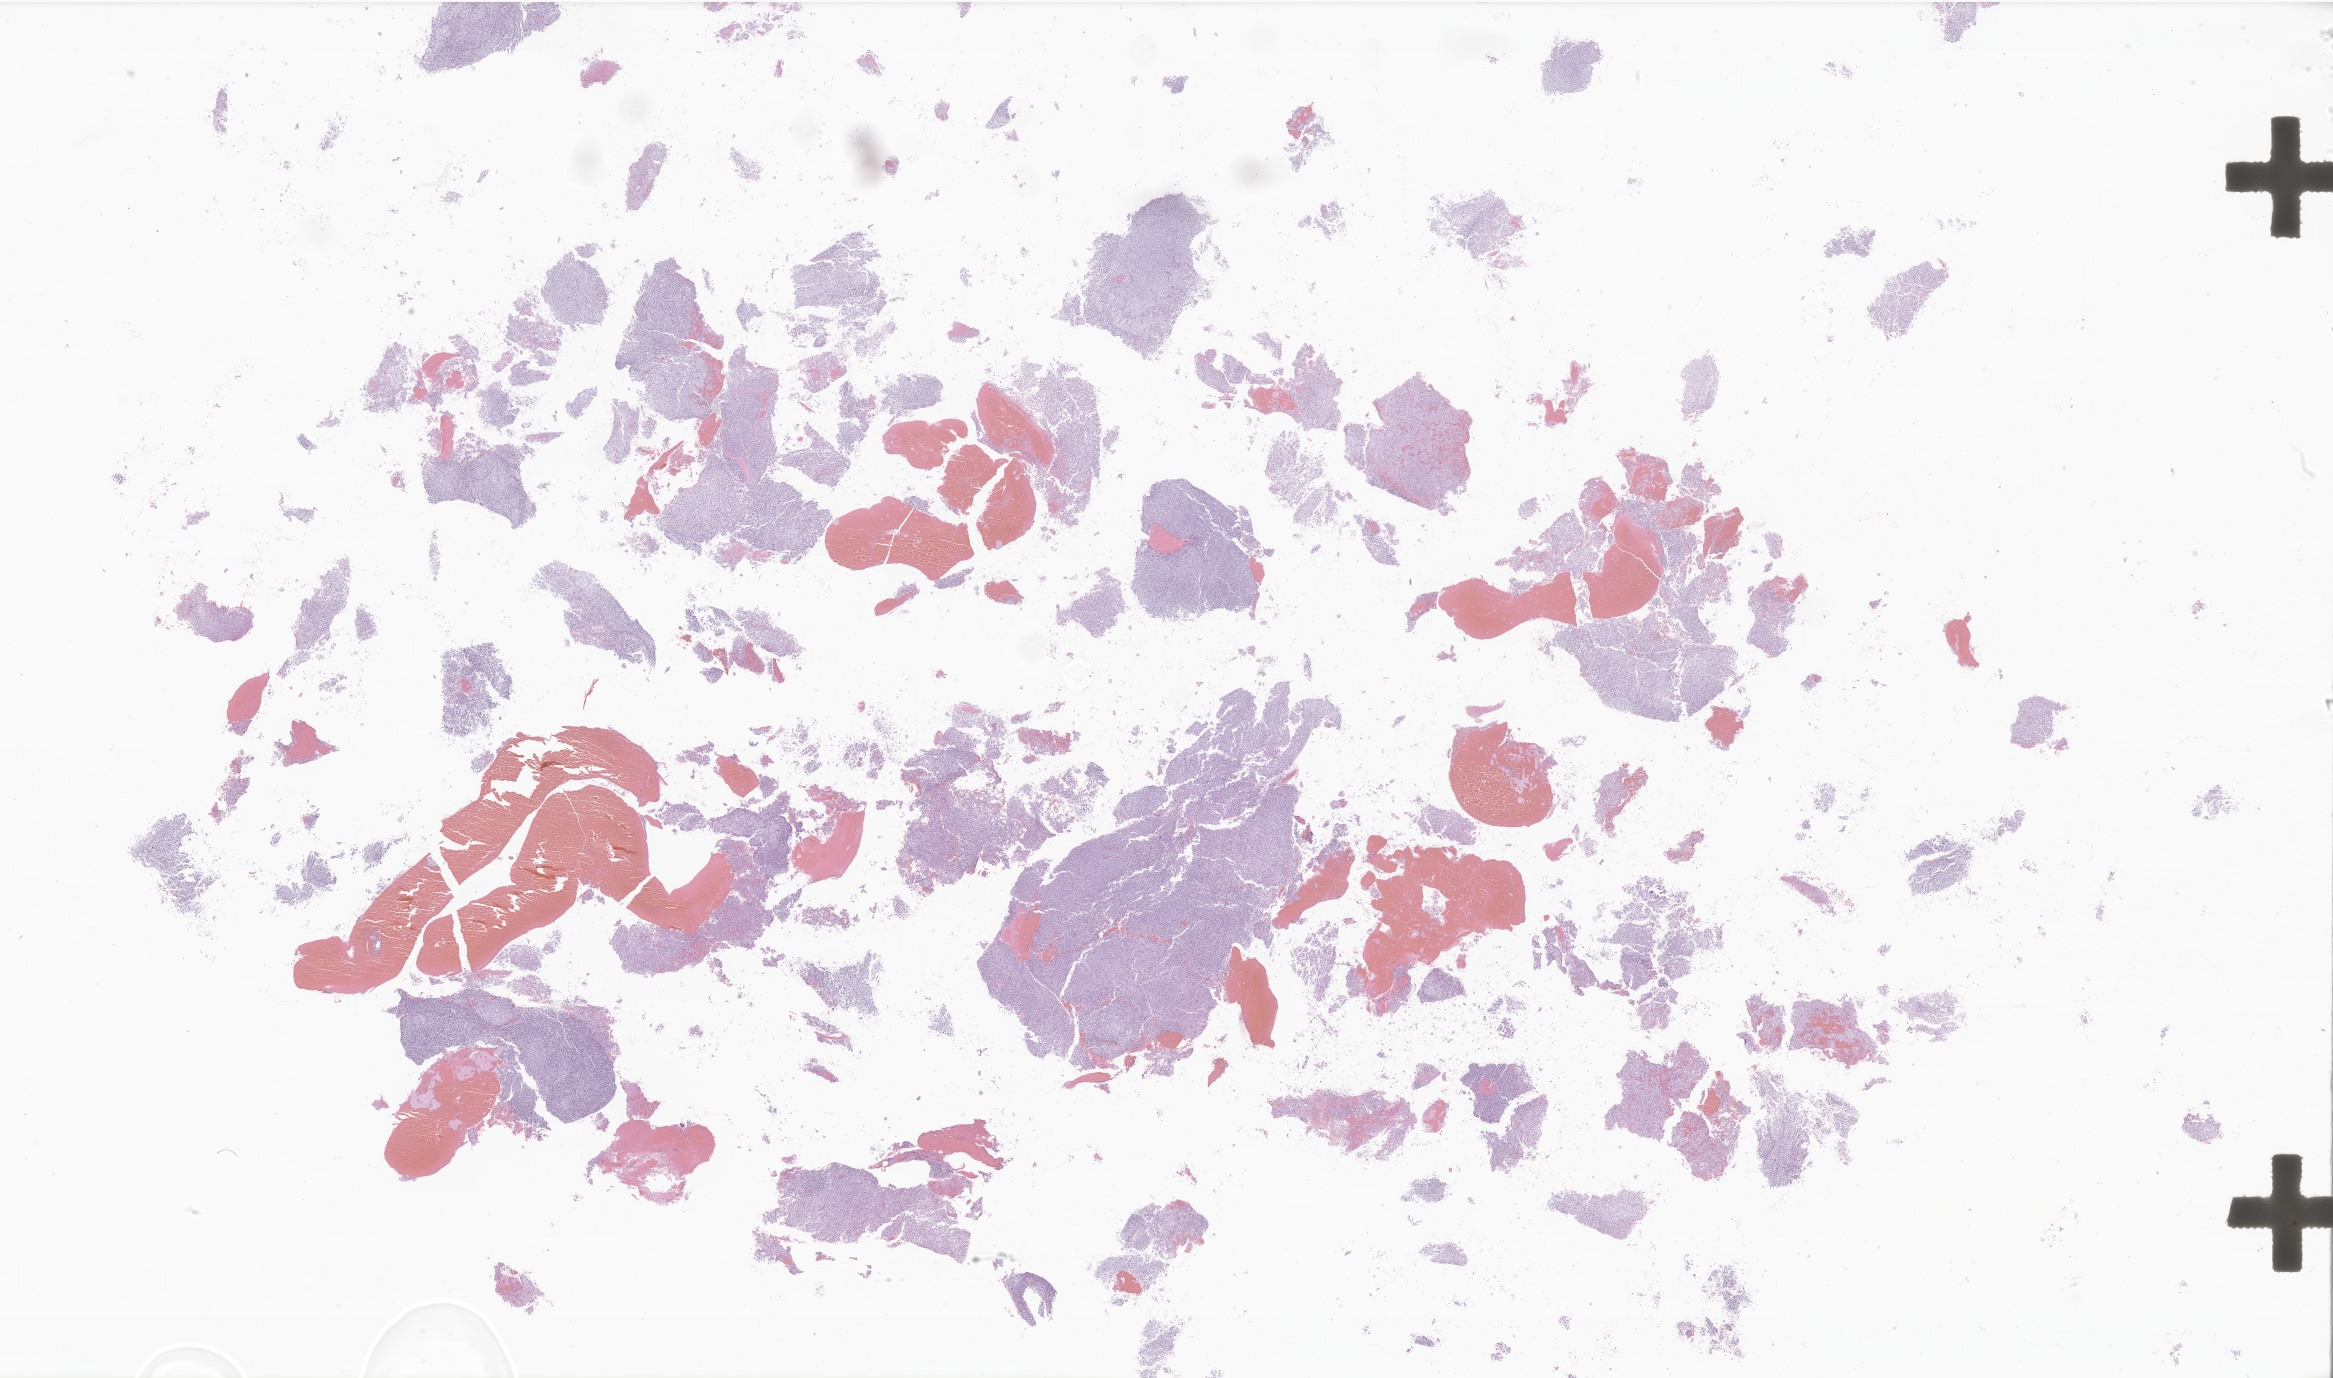
Digitized hematoxylin and eosin (H&E)-stained section of tumor tissue from the brain — low-resolution overview of the scanned area, about 39.3 x 23.2 mm, formalin-fixed paraffin-embedded section. Patient: male, age 96 months (8 years).
Diagnosis: Neoplasm, malignant.